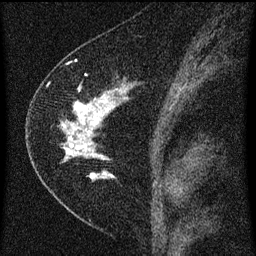
Breast MRI (dynamic contrast-enhanced), one sagittal slice. Slice 36 of 60 in the series (ordered by position). Dynamic contrast-enhanced series, image 2 of 3 at this slice position (ordered by acquisition). 1.5 T. TE 4.2 ms, TR 8 ms. 2 mm slice thickness. 256 × 256 image matrix. Patient: female, 47 years.
Structures marked on this image (semi-automatically segmented with operator editing):
- analysis volume of interest (the breast-tissue region the enhancement analysis was run in; not a lesion): bounding box (x1, y1, x2, y2) in pixels: (38, 76, 135, 193)
- tumour enhancement mask (voxels above the 70 % enhancement threshold inside the analysis volume of interest): (61, 90, 123, 179)